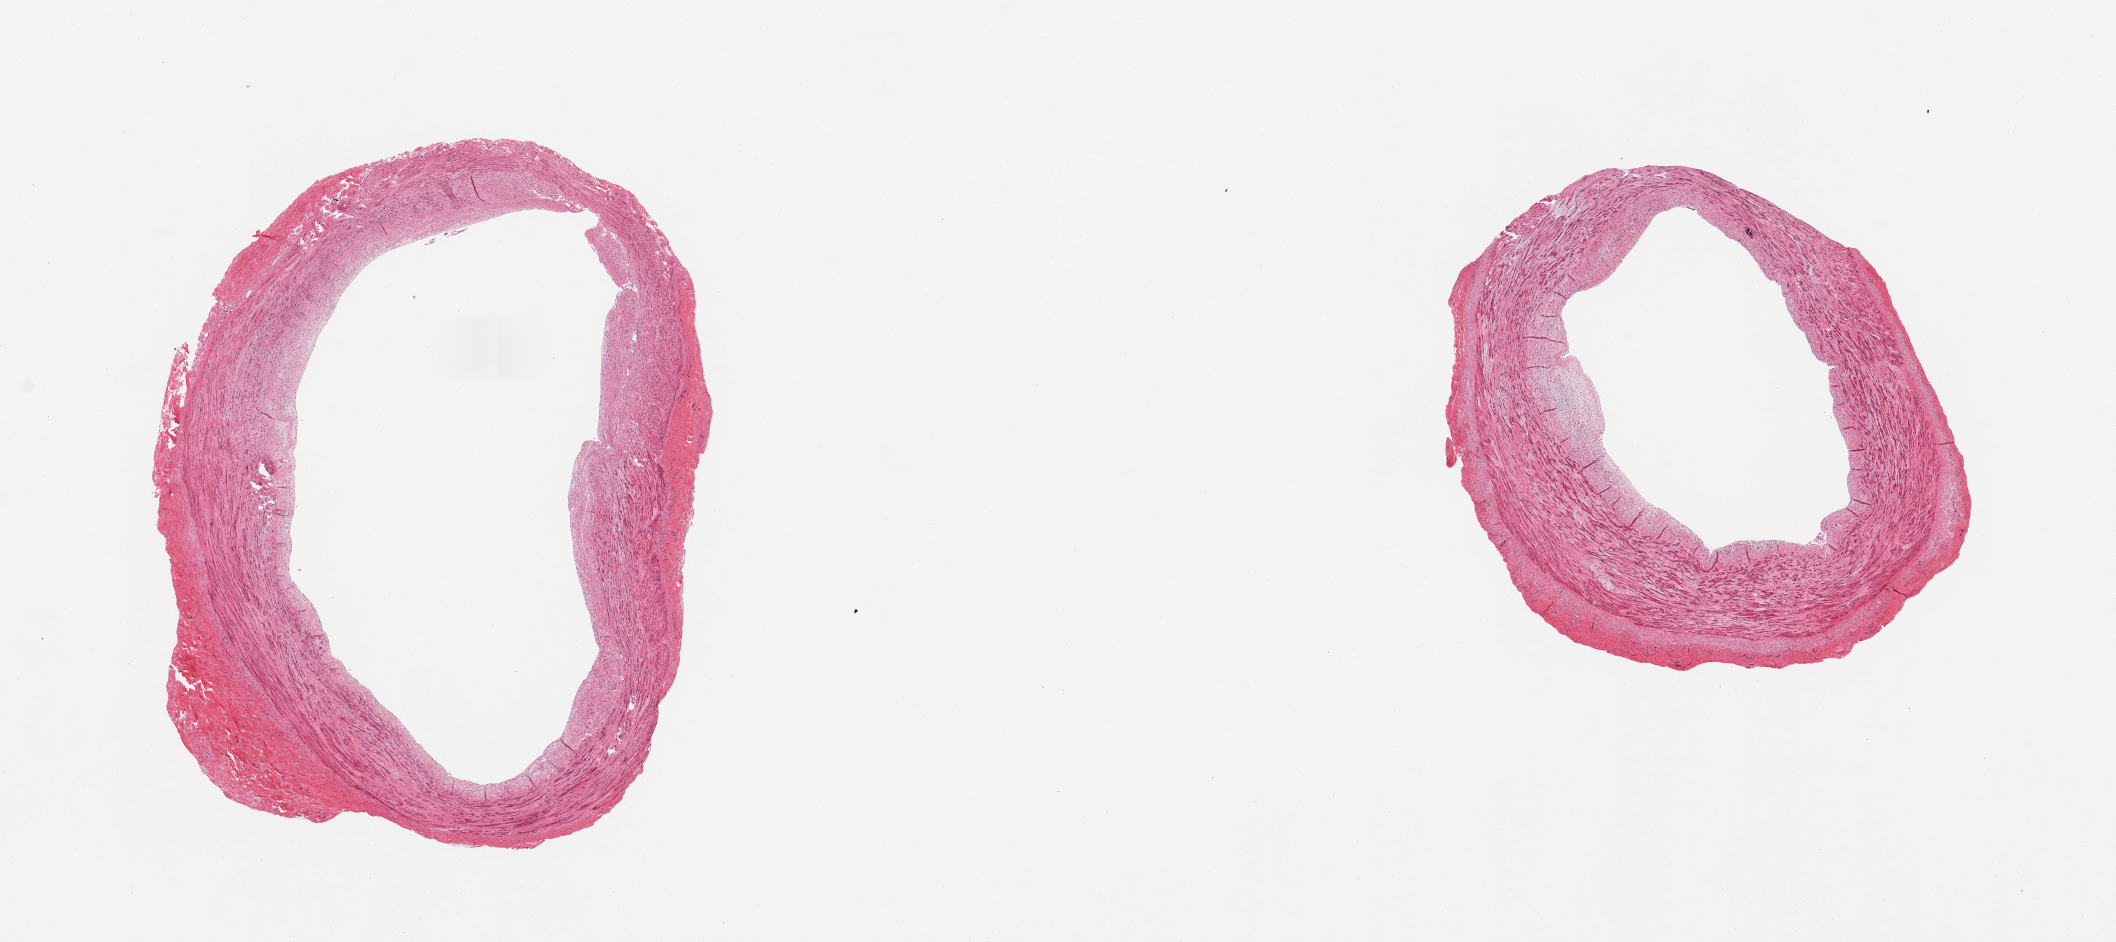
Digitized haematoxylin and eosin-stained section, shown as a low-resolution overview of the whole scanned area (about 16.7 x 7.5 mm, slide scanned at 20x); PAXgene-fixed paraffin-embedded (PFPE) section; section of tibial artery (target tissue); donor tissue sample. Female donor.
Reviewer comment on this tissue sample: 2 pieces, clean specimen, no atherosis.